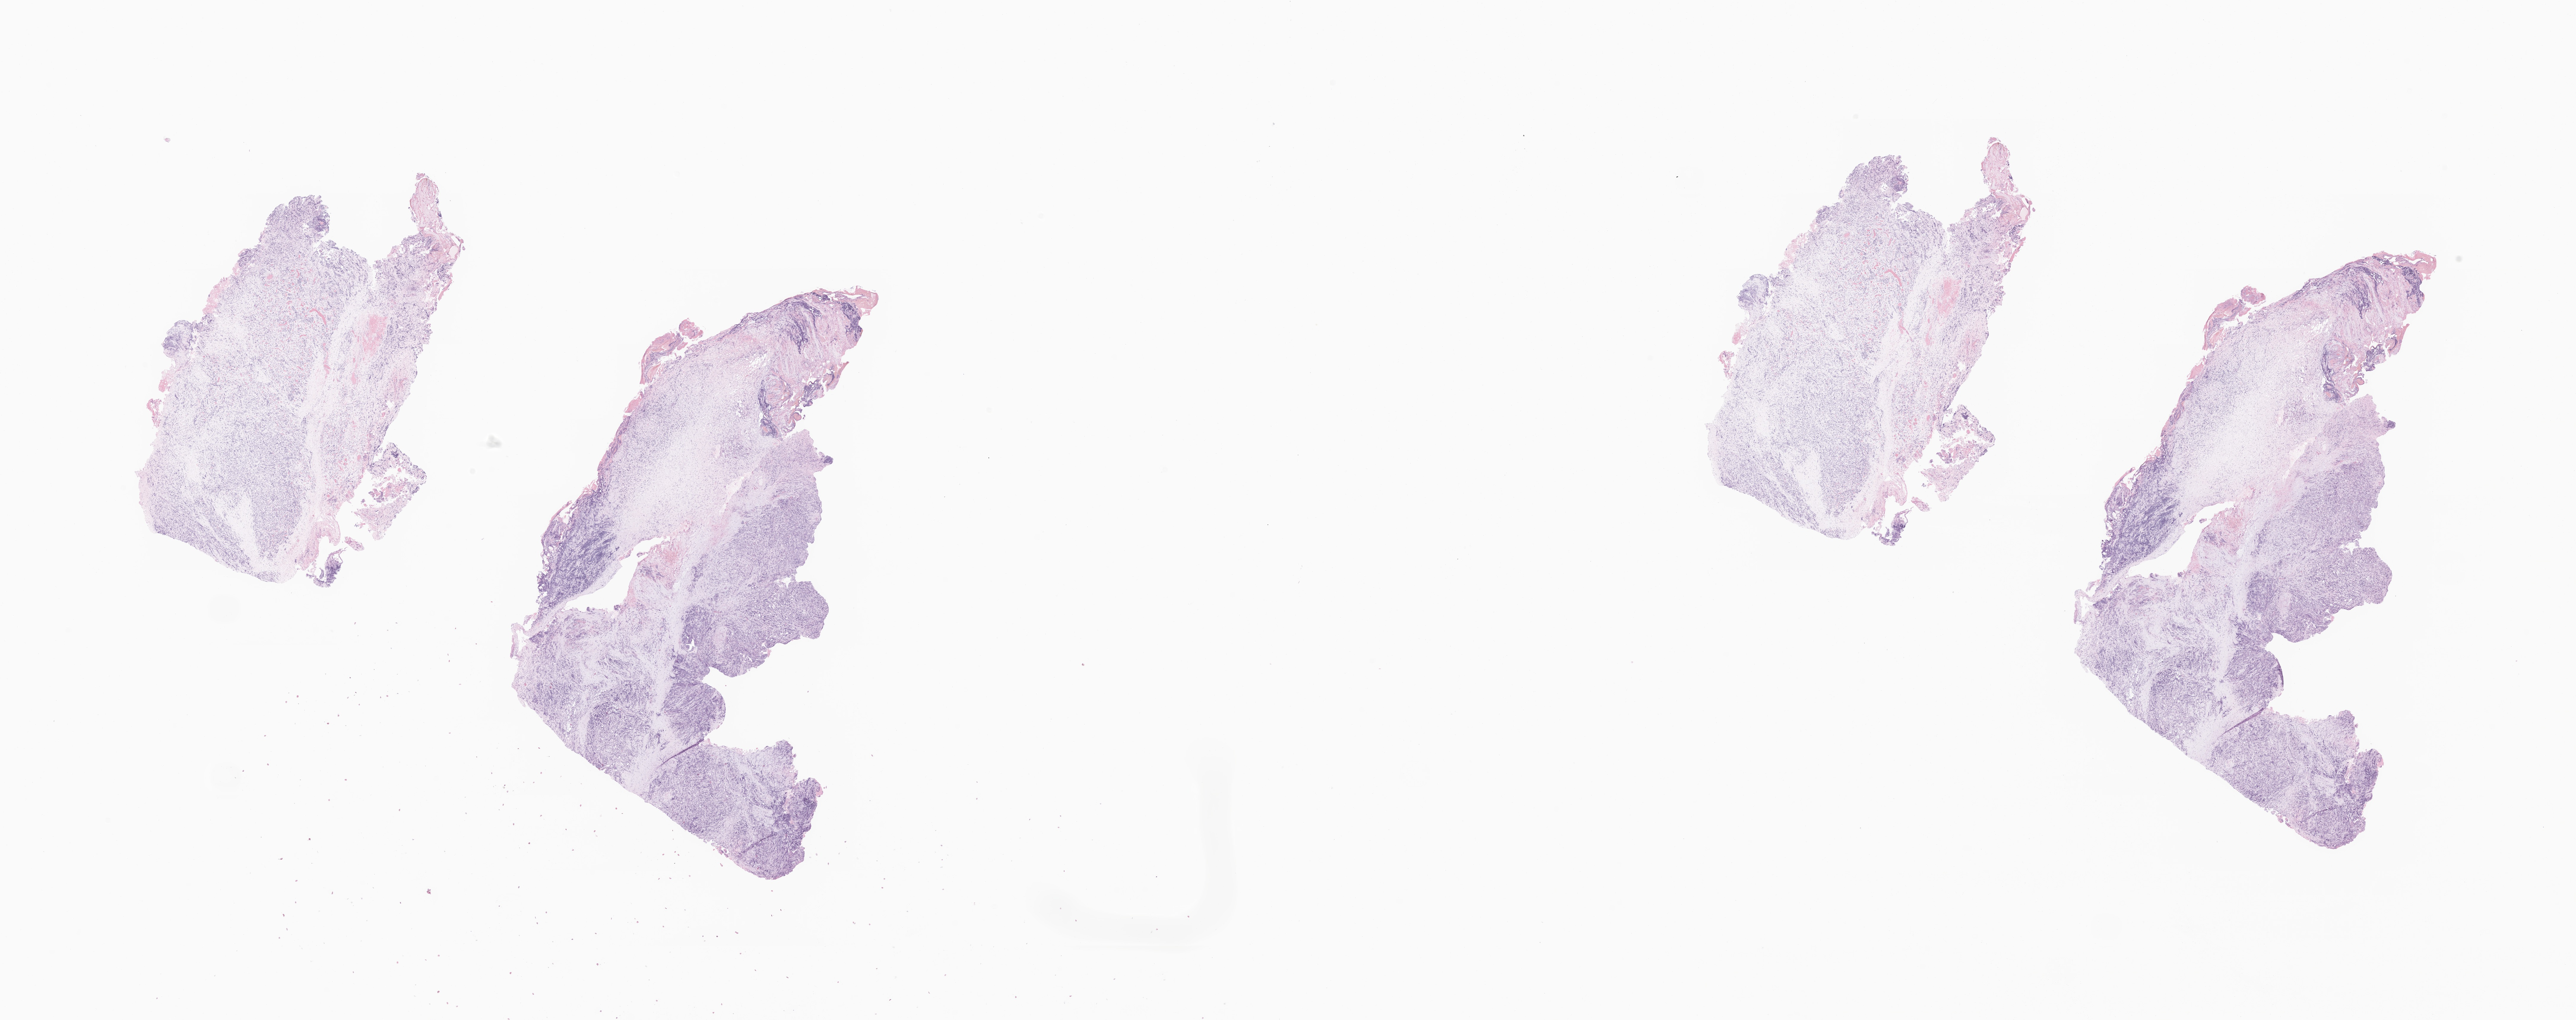
Hematoxylin and eosin (H&E) whole-slide image of tumor tissue from the adrenal gland, whole scanned area (about 36.6 x 14.5 mm) shown as a low-resolution overview, formalin-fixed, paraffin-embedded (FFPE) tissue. Female patient, age 50 months (4 years 2 months).
• recorded diagnosis: Neuroblastoma, NOS